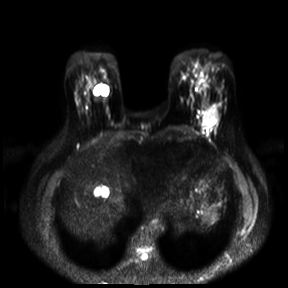
Breast MRI, one axial slice. Slice 7 of 30 in the series (ordered by position). Diffusion-weighted series; image 2 of 4 stored at this slice position (different b-values; order by instance number). 3 T. 4 mm slice thickness. 288 × 288 image matrix. Female patient.
Outlined on this slice (outlined manually by an expert reader):
- tumour on diffusion-weighted imaging: bounding box <204,108,217,126> (left, top, right, bottom; pixels)